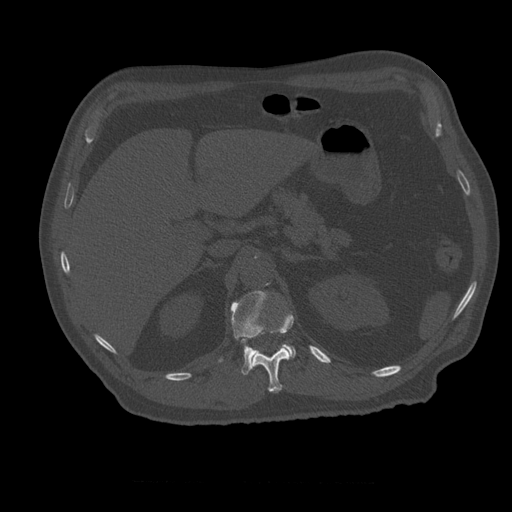
CT including the spine, one axial slice. Position 252 of 399 along the scan axis. Bone window (W 1800 / L 400 HU). 512 × 512 image matrix. Patient age 73 years. Case-level facts recorded for this patient, not image findings: primary cancer: prostate; vertebrae with lytic lesions (as recorded): L2.
Annotated regions visible in this slice (semi-automatically segmented with operator editing):
- L1 vertebra: bounding box [x1, y1, x2, y2] px = [219, 291, 296, 375]
- T12 vertebra: [252, 313, 294, 393]